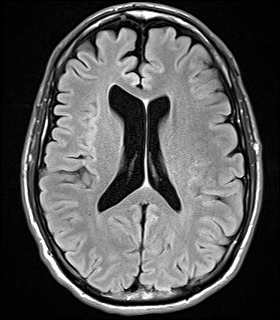
Brain MRI from a brain-tumour surgery series, one axial slice. Slice 14 of 32 in the series (ordered by position). T2 FLAIR. 5 mm slice thickness. 280 × 320 image matrix, field of view 184 × 210 mm. Case-level facts recorded for this patient, not image findings: histopathology: Glial fibroma; tumour location: Right Frontal.
Structures marked on this image (outlined manually by an expert reader):
- tumour: box from (x=124, y=75) to (x=130, y=77) px